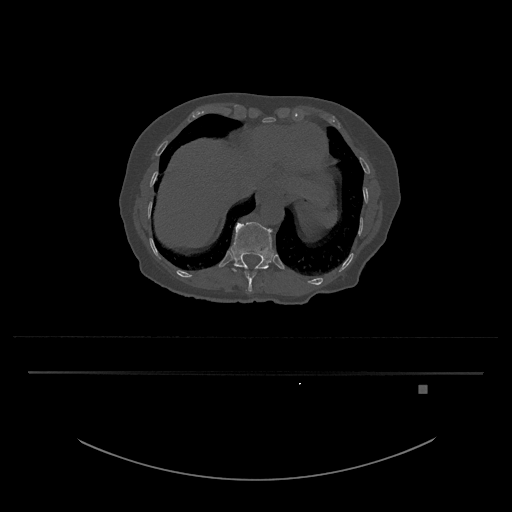
CT including the spine, one axial slice; position 632 of 797 along the scan axis; 120 kVp; bone window (W 1800 / L 400 HU); 0.5 mm slice thickness; 512 × 512 image matrix. Patient: female, 57 years. Case-level facts recorded for this patient, not image findings: primary cancer: cervical.
Structures marked on this image (semi-automatically segmented with operator editing):
- T11 vertebra: bounding box [x1, y1, x2, y2] px = [245, 267, 263, 292]
- T12 vertebra: [231, 222, 274, 272]